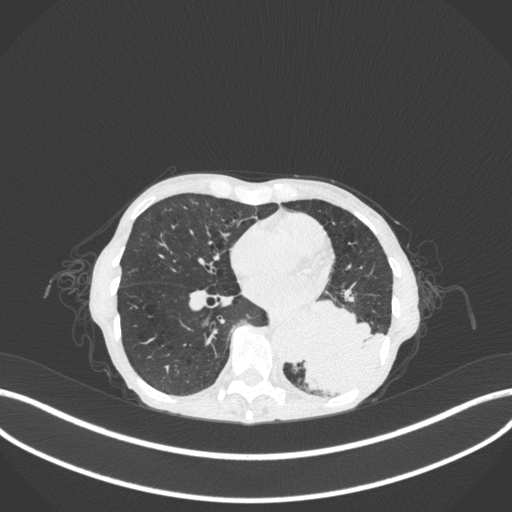
Chest CT, one axial slice. Slice 113 of 347 in the series (ordered by position). 120 kVp. Lung window (W 1500 / L -600 HU). 1 mm slice thickness. 512 × 512 image matrix, field of view 400 × 400 mm. Patient: female, 70 years. From the clinical record (not read from this slice): clinical TNM (as recorded): T3 N0 M0; histopathological grade: G3.
Outlined on this slice (rectangle marked by the reading radiologist):
- lung tumour (recorded histology: small cell carcinoma): bounding box [x1, y1, x2, y2] px = [295, 290, 389, 397]